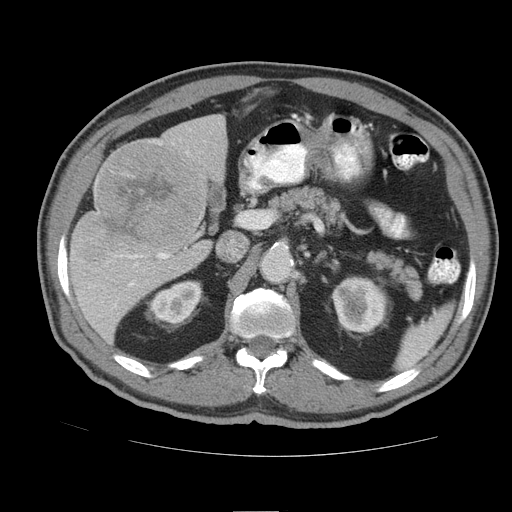
Contrast-enhanced abdominal CT (liver protocol), one axial slice; slice 48 of 105 in the series (ordered by position); reconstruction kernel STANDARD; soft-tissue window (W 400 / L 40 HU); 2.5 mm slice thickness; 512 × 512 image matrix, field of view 380 × 380 mm. From the clinical record (not read from this slice): diagnosis: hepatocellular carcinoma (patient treated with transarterial chemoembolisation; whether this scan precedes or follows treatment is not stated here); TNM stage (as recorded): Stage-IIIB; Child-Pugh class: A; tumour nodularity: multinodular.
Structures marked on this image (semi-automatic segmentation, software-assisted and operator-edited):
- liver parenchyma outside the tumour (the mass and vessels are separate outlines, so this box may not span the whole liver): box from (x=68, y=114) to (x=227, y=342) px
- mass: (x=72, y=141)–(x=200, y=259)
- liver vessels: (x=108, y=152)–(x=188, y=307)